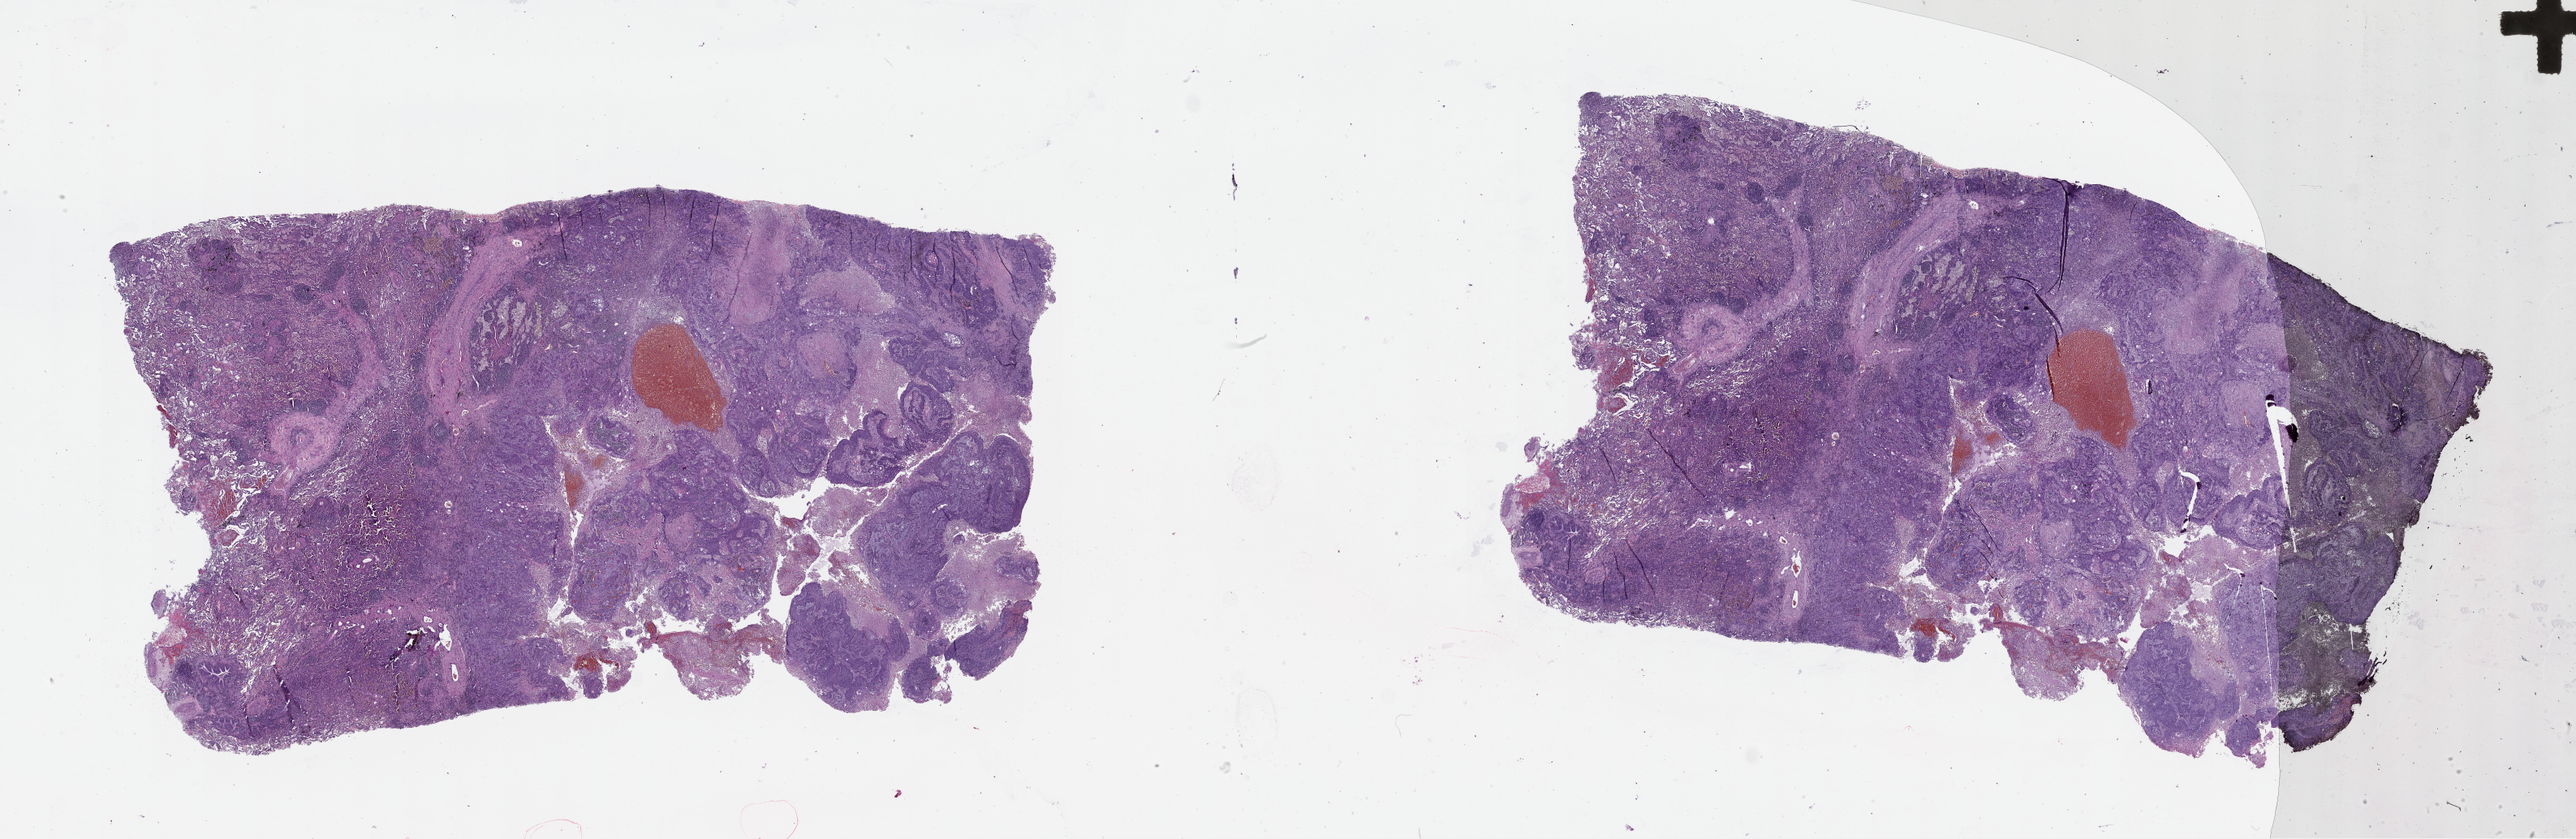
Digitized H&E tissue section (whole slide), shown as a low-resolution overview of the whole scanned area (about 51.1 x 16.7 mm); lung, tumour tissue. Male, 57 y/o.
Patient diagnosis (cohort enrolment): squamous cell carcinoma (lung).